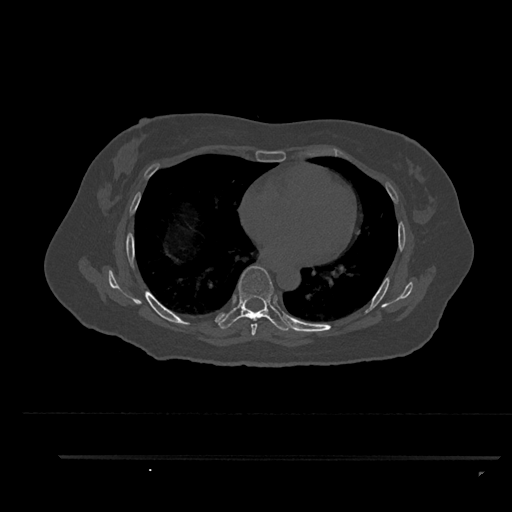
CT including the spine, one axial slice; slice 520 of 797 in the series (ordered by position); reconstruction kernel Br40s/3; 120 kVp; bone window (W 1800 / L 400 HU); 0.5 mm slice thickness; 512 × 512 image matrix. Female patient, age 44 years. Case-level facts recorded for this patient, not image findings: primary cancer: renal; vertebrae with lytic lesions (as recorded): L1.
Annotated regions visible in this slice (semi-automatic segmentation, software-assisted and operator-edited):
- T6 vertebra: box from (x=249, y=318) to (x=258, y=336) px
- T7 vertebra: (x=218, y=266)–(x=294, y=331)